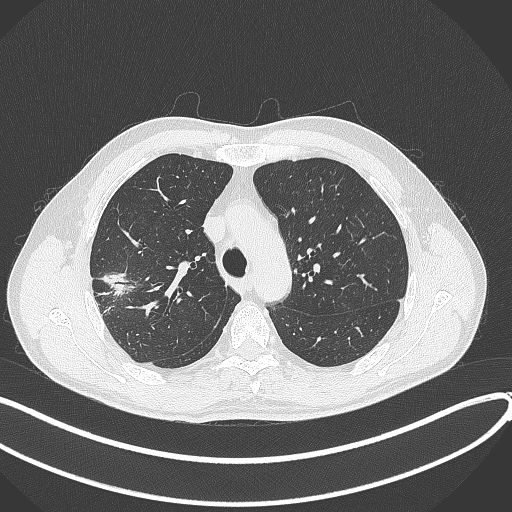
Chest CT, one axial slice; position 306 of 381 along the scan axis; reconstruction kernel B70f; lung window (W 1500 / L -600 HU); 1 mm slice thickness; 512 × 512 image matrix, field of view 400 × 400 mm. Male patient, age 62 years. Case-level facts recorded for this patient, not image findings: clinical TNM (as recorded): T1c N0 M0; histopathological grade: G2-3.
Structures marked on this image (bounding box drawn by a radiologist):
- lung tumour (recorded histology: adenocarcinoma): bounding box (x1, y1, x2, y2) in pixels: (99, 268, 137, 298)